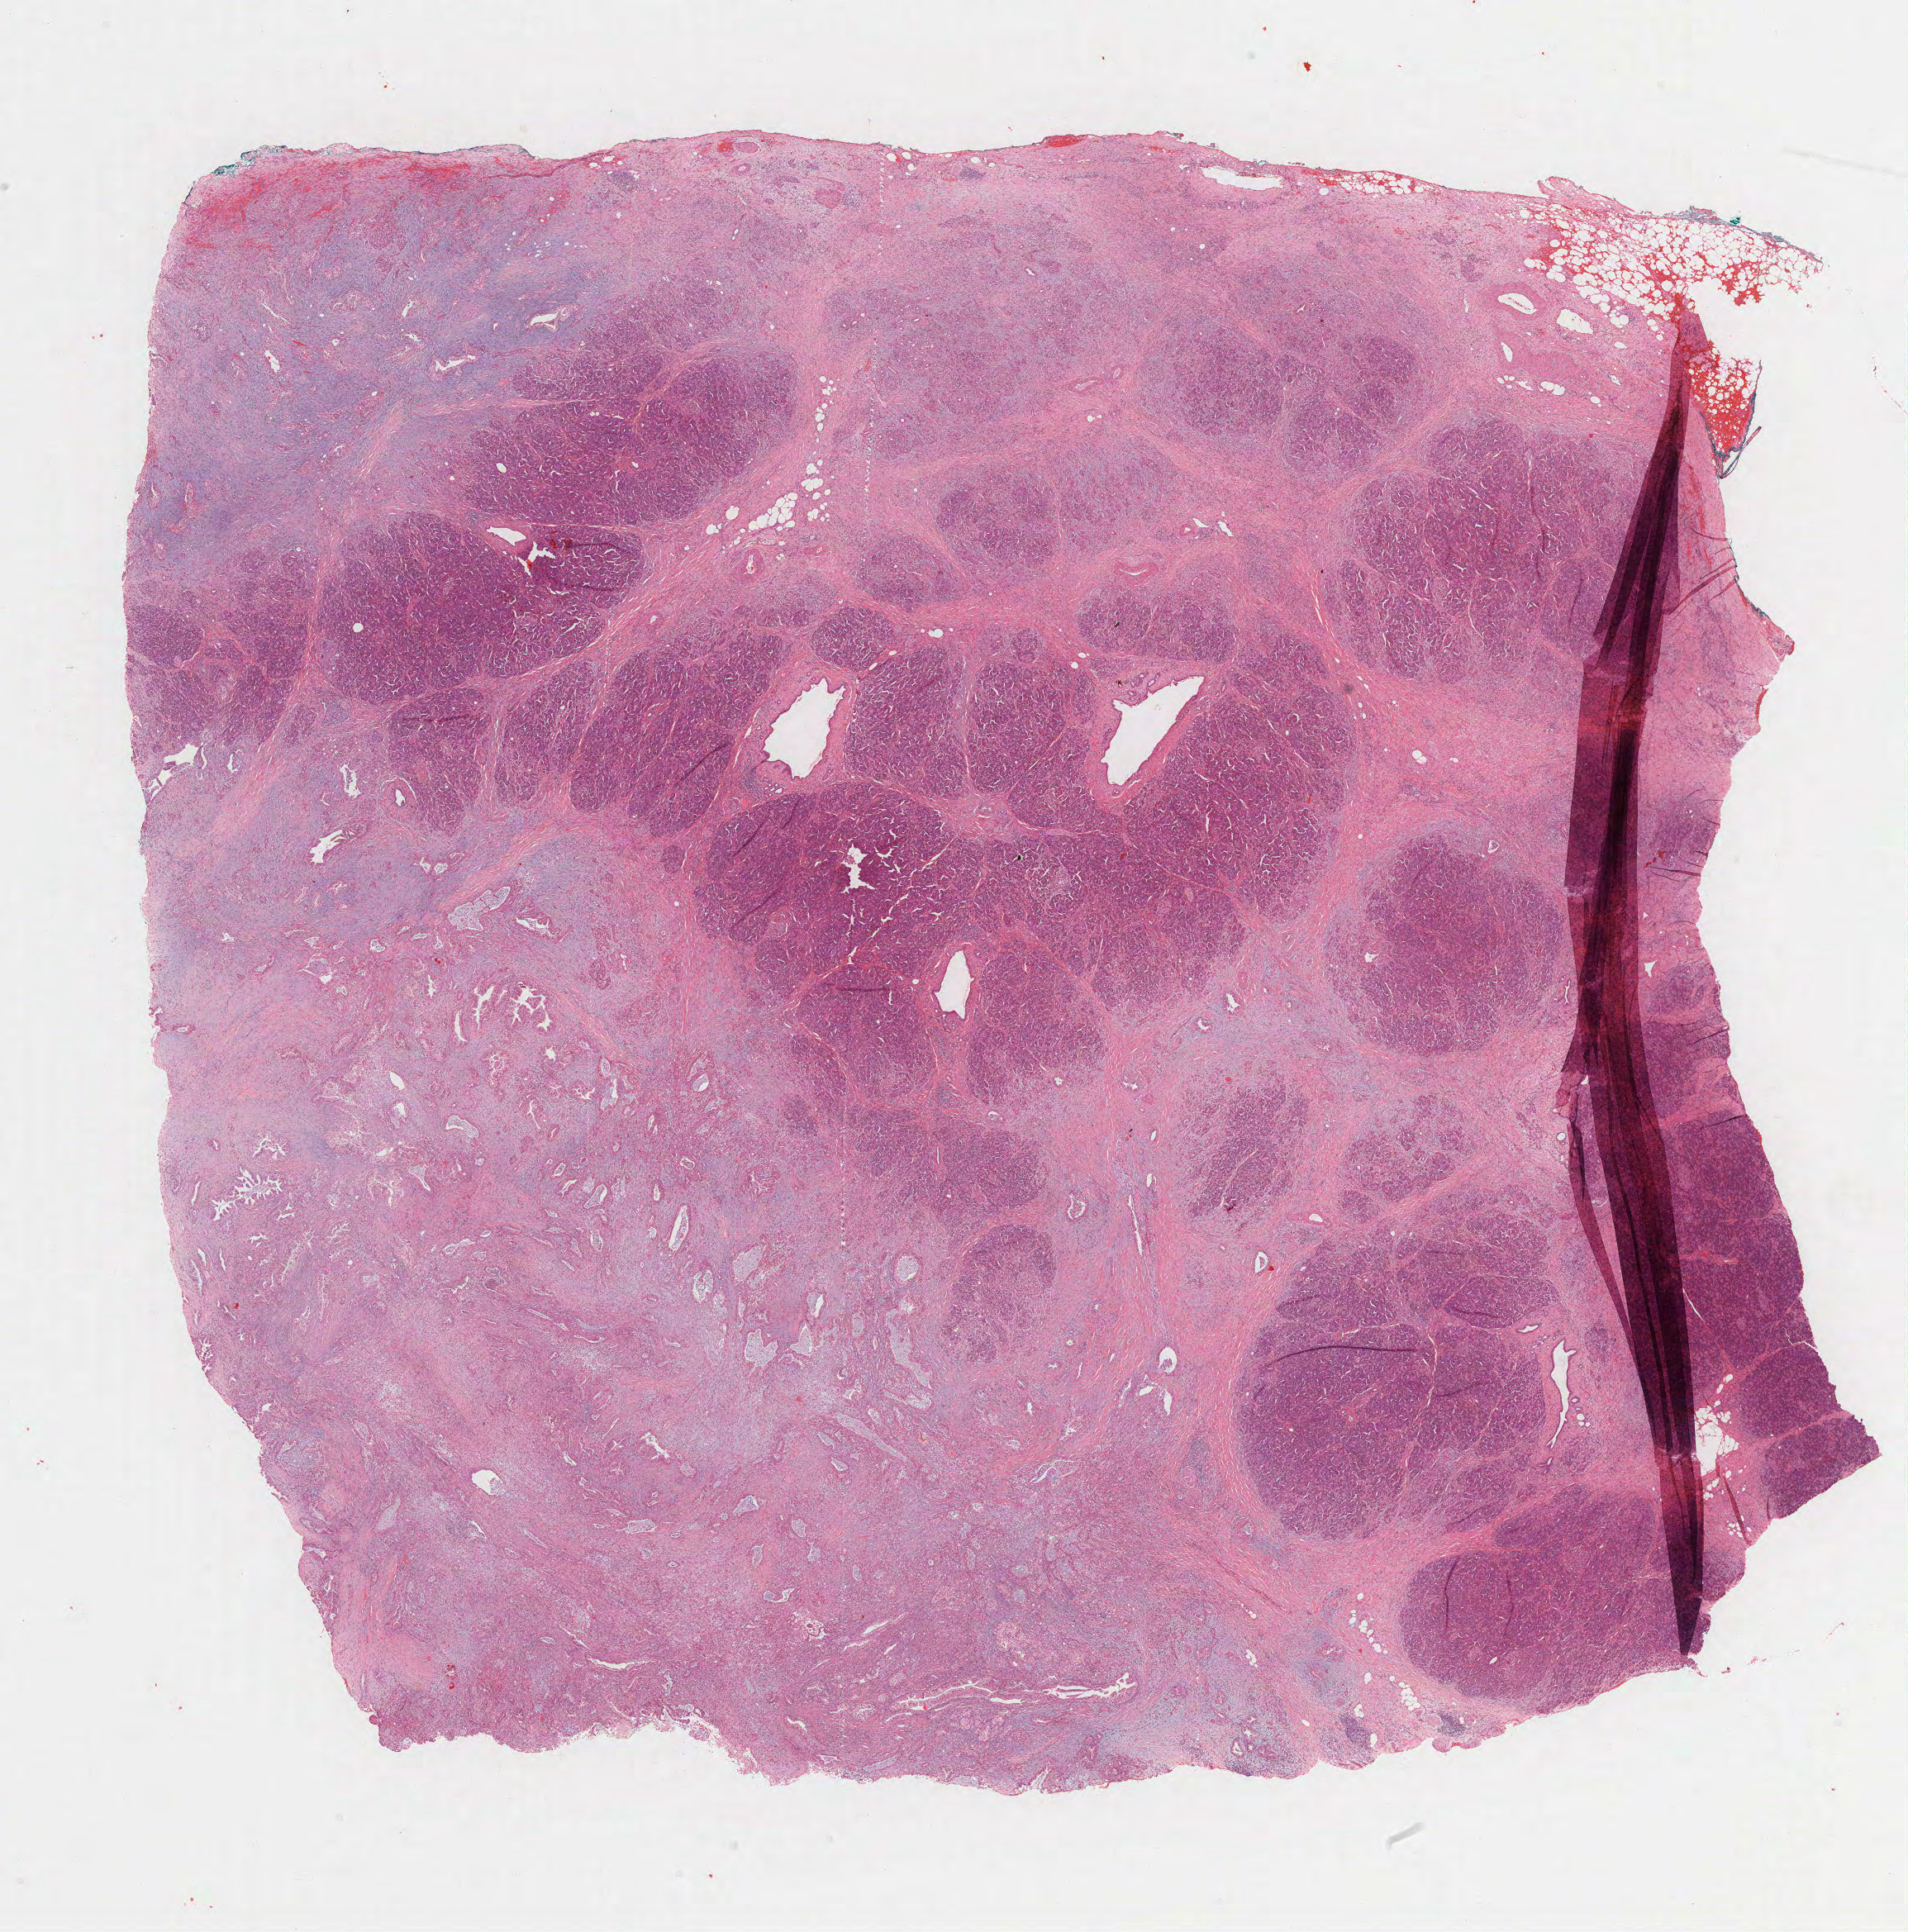
Whole-slide histology image, H&E — whole scanned area (about 18.7 x 18.9 mm, acquisition: 40x scan) shown as a low-resolution overview. Formalin-fixed paraffin-embedded (FFPE) diagnostic section. Pancreas, primary tumour sample. Female, age 61 years at initial diagnosis. Histologic grade: G2 (moderately differentiated).
Histologic diagnosis: Infiltrating duct carcinoma, NOS (head of pancreas). AJCC pathologic stage: IIB (7th edition).